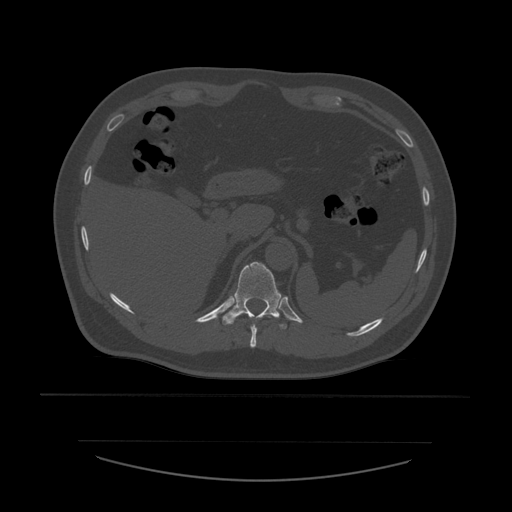
CT including the spine, one axial slice; position 281 of 532 along the scan axis; reconstruction kernel STANDARD; 120 kVp; bone window (W 1800 / L 400 HU); 1.25 mm slice thickness; 512 × 512 image matrix. Patient age 44 years. From the clinical record (not read from this slice): primary cancer: soft tissue sarcoma.
Outlined on this slice (semi-automatically segmented with operator editing):
- T10 vertebra: bounding box (x1, y1, x2, y2) in pixels: (250, 324, 258, 348)
- T11 vertebra: (223, 262, 287, 329)